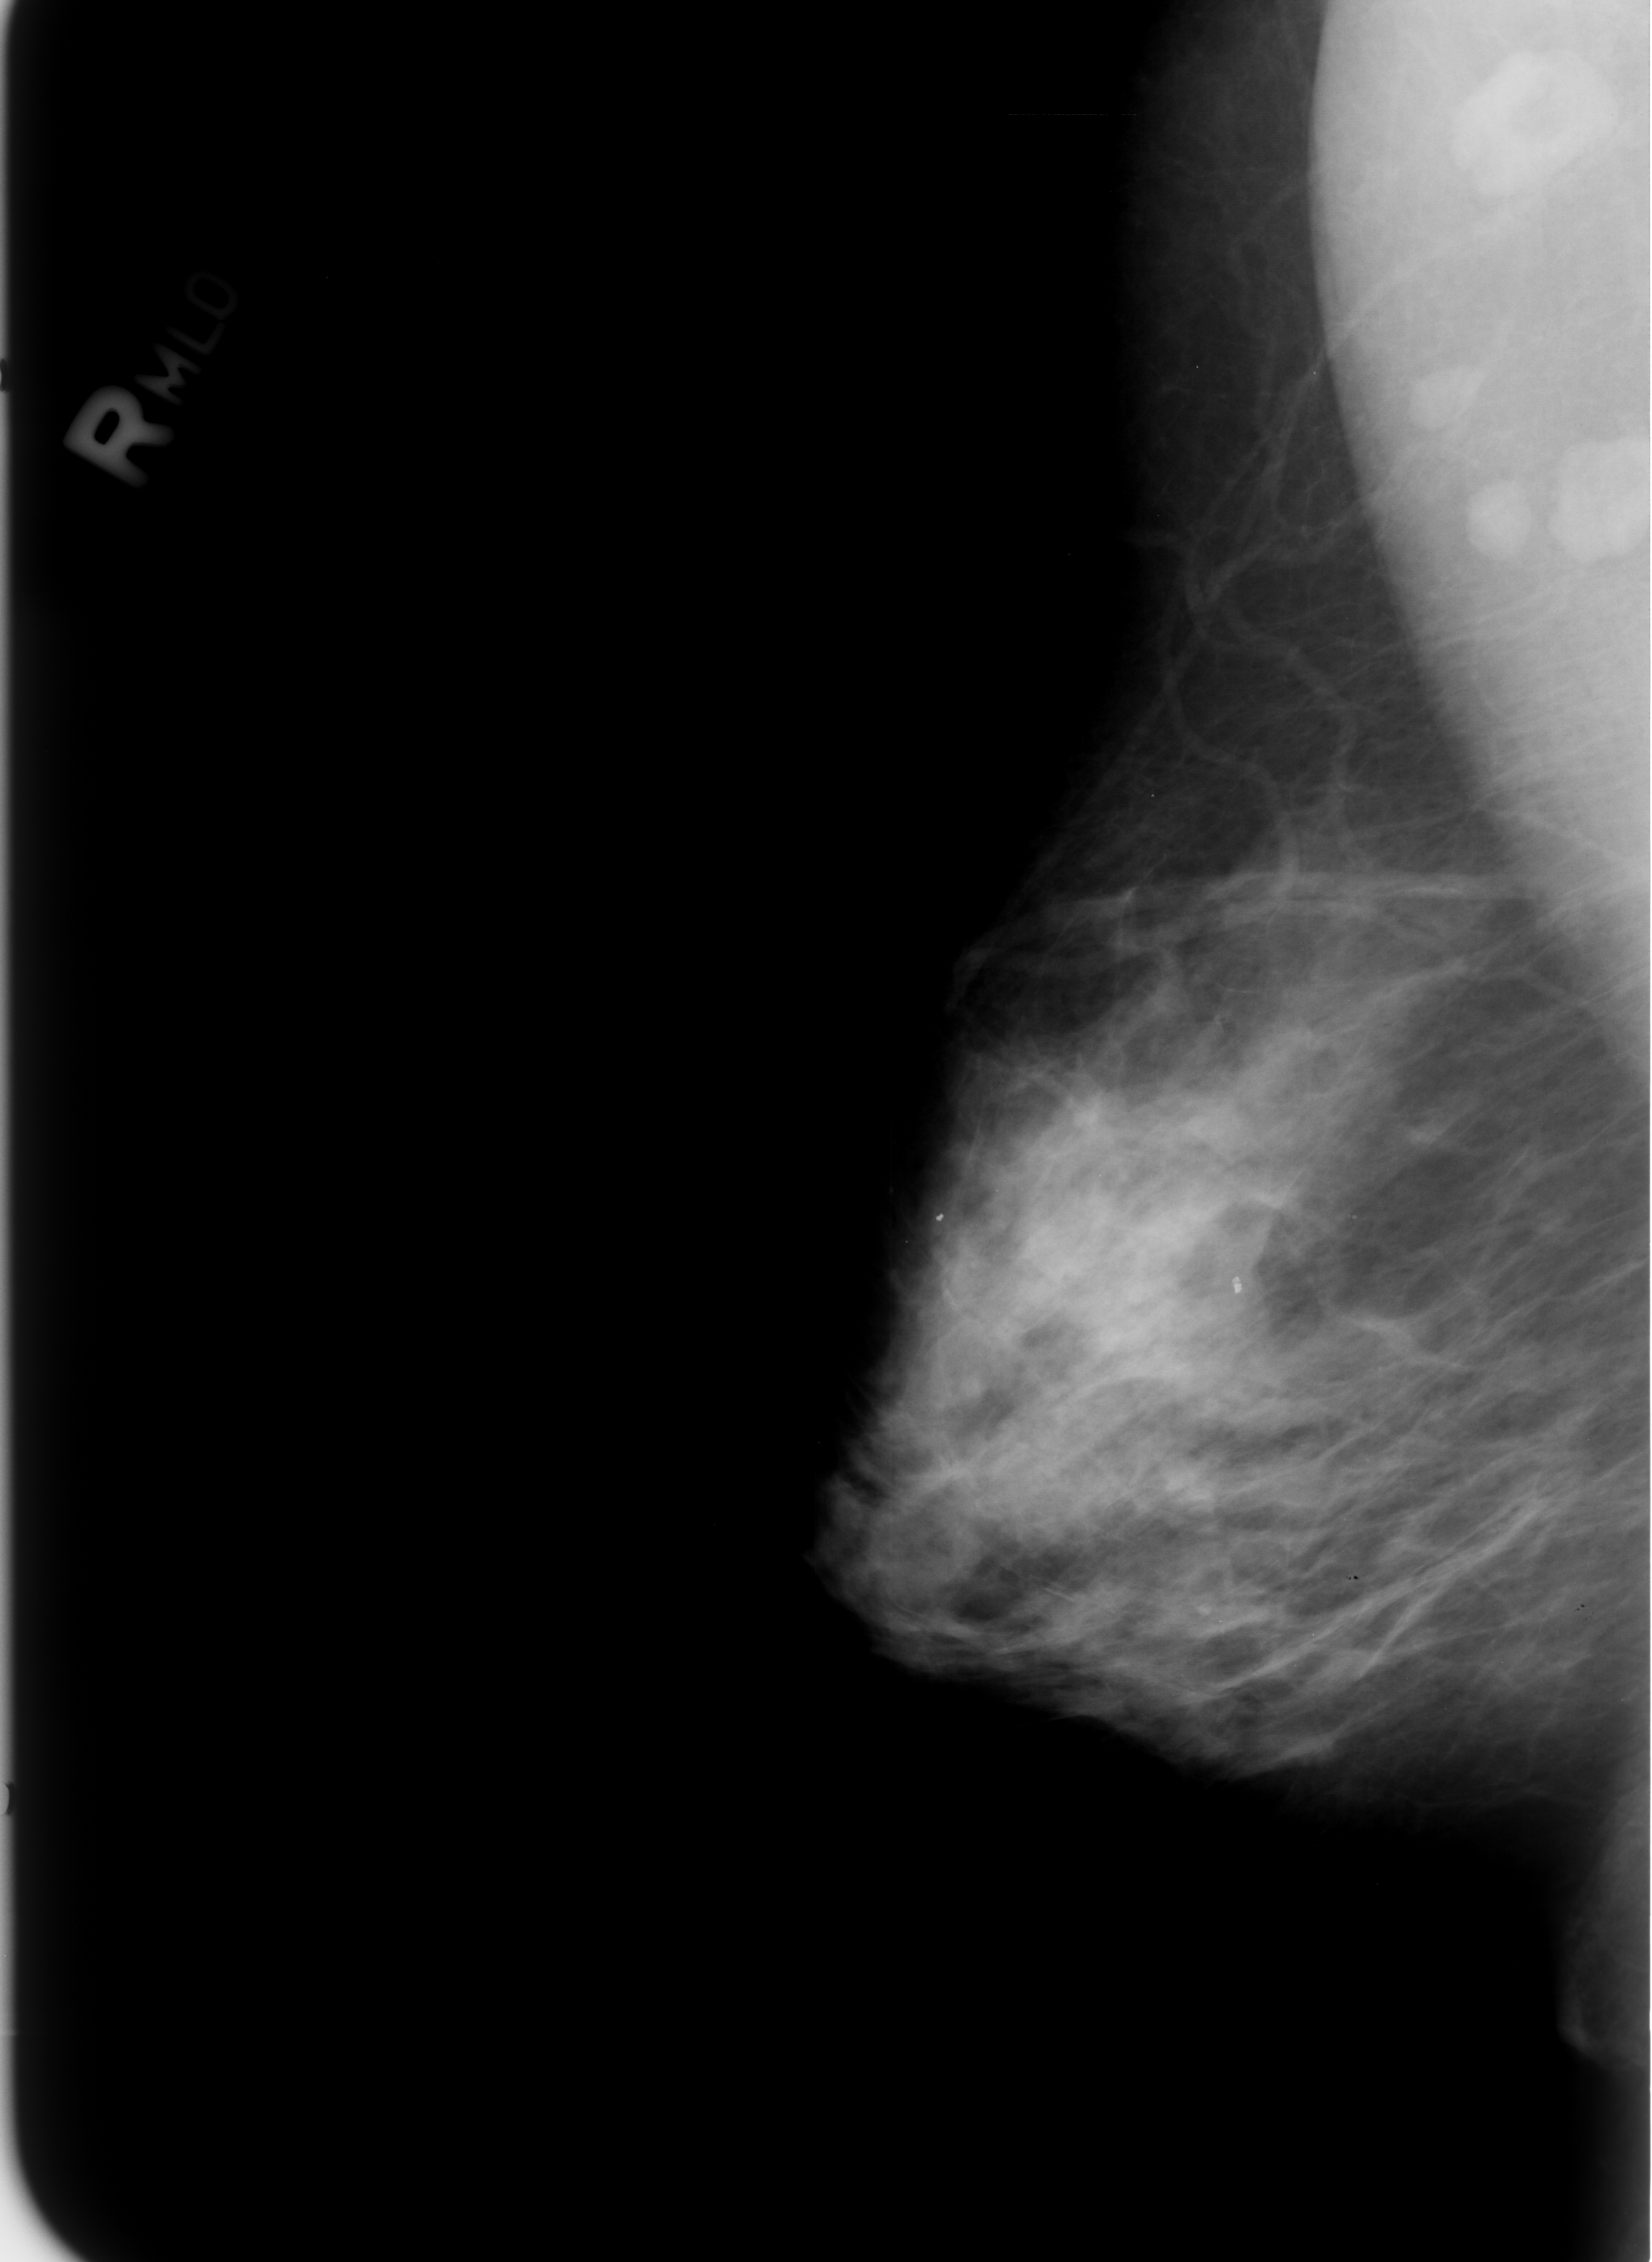
Digitized screen-film mammogram; right breast; mediolateral oblique (MLO) view; BI-RADS breast density category 3 (scale 1–4); 1652 × 2262 image matrix.
Marked abnormalities (boxes around the expert regions of interest):
- Finding 1 of 2: calcifications, morphology lucent center; BI-RADS assessment category 2; benign; no additional work-up was recommended (outcome (as recorded, no biopsy): benign without callback): bounding box [x1, y1, x2, y2] px = [905, 1194, 975, 1257]
- Finding 2 of 2: calcifications, morphology lucent center; BI-RADS assessment category 2; benign; no additional work-up was recommended (outcome (as recorded, no biopsy): benign without callback): [1210, 1259, 1289, 1328]